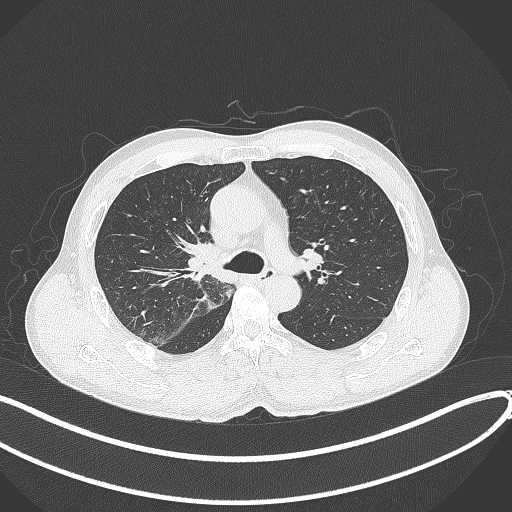
Chest CT, one axial slice; reconstruction kernel B70f; lung window (W 1500 / L -600 HU); 1 mm slice thickness; 512 × 512 image matrix, field of view 400 × 400 mm. Patient: male, 53 years. Case-level facts recorded for this patient, not image findings: clinical TNM (as recorded): T1b N0 M0.
Annotated regions visible in this slice (bounding box drawn by a radiologist):
- lung tumour (recorded histology: squamous cell carcinoma): bounding box <181,235,228,278> (left, top, right, bottom; pixels)